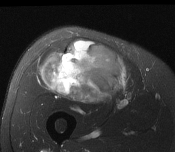
MRI of an extremity soft-tissue mass, one axial slice. Position 82 of 116 along the scan axis. T2-weighted fat-saturated. MR volume resampled by the dataset authors to the PET/CT grid (not the native acquisition matrix). 175 × 152 image matrix. Male patient. Case-level facts recorded for this patient, not image findings: histological type: pleiomorphic leiomyosarcoma; grade: intermediate; site of the primary tumour: right thigh.
Structures marked on this image (expert contour drawn on MRI and transferred to this co-registered scan by the dataset authors):
- gross tumour volume including surrounding oedema: bounding box (x1, y1, x2, y2) in pixels: (42, 40, 128, 103)
- gross tumour volume (mass): (42, 40, 128, 103)